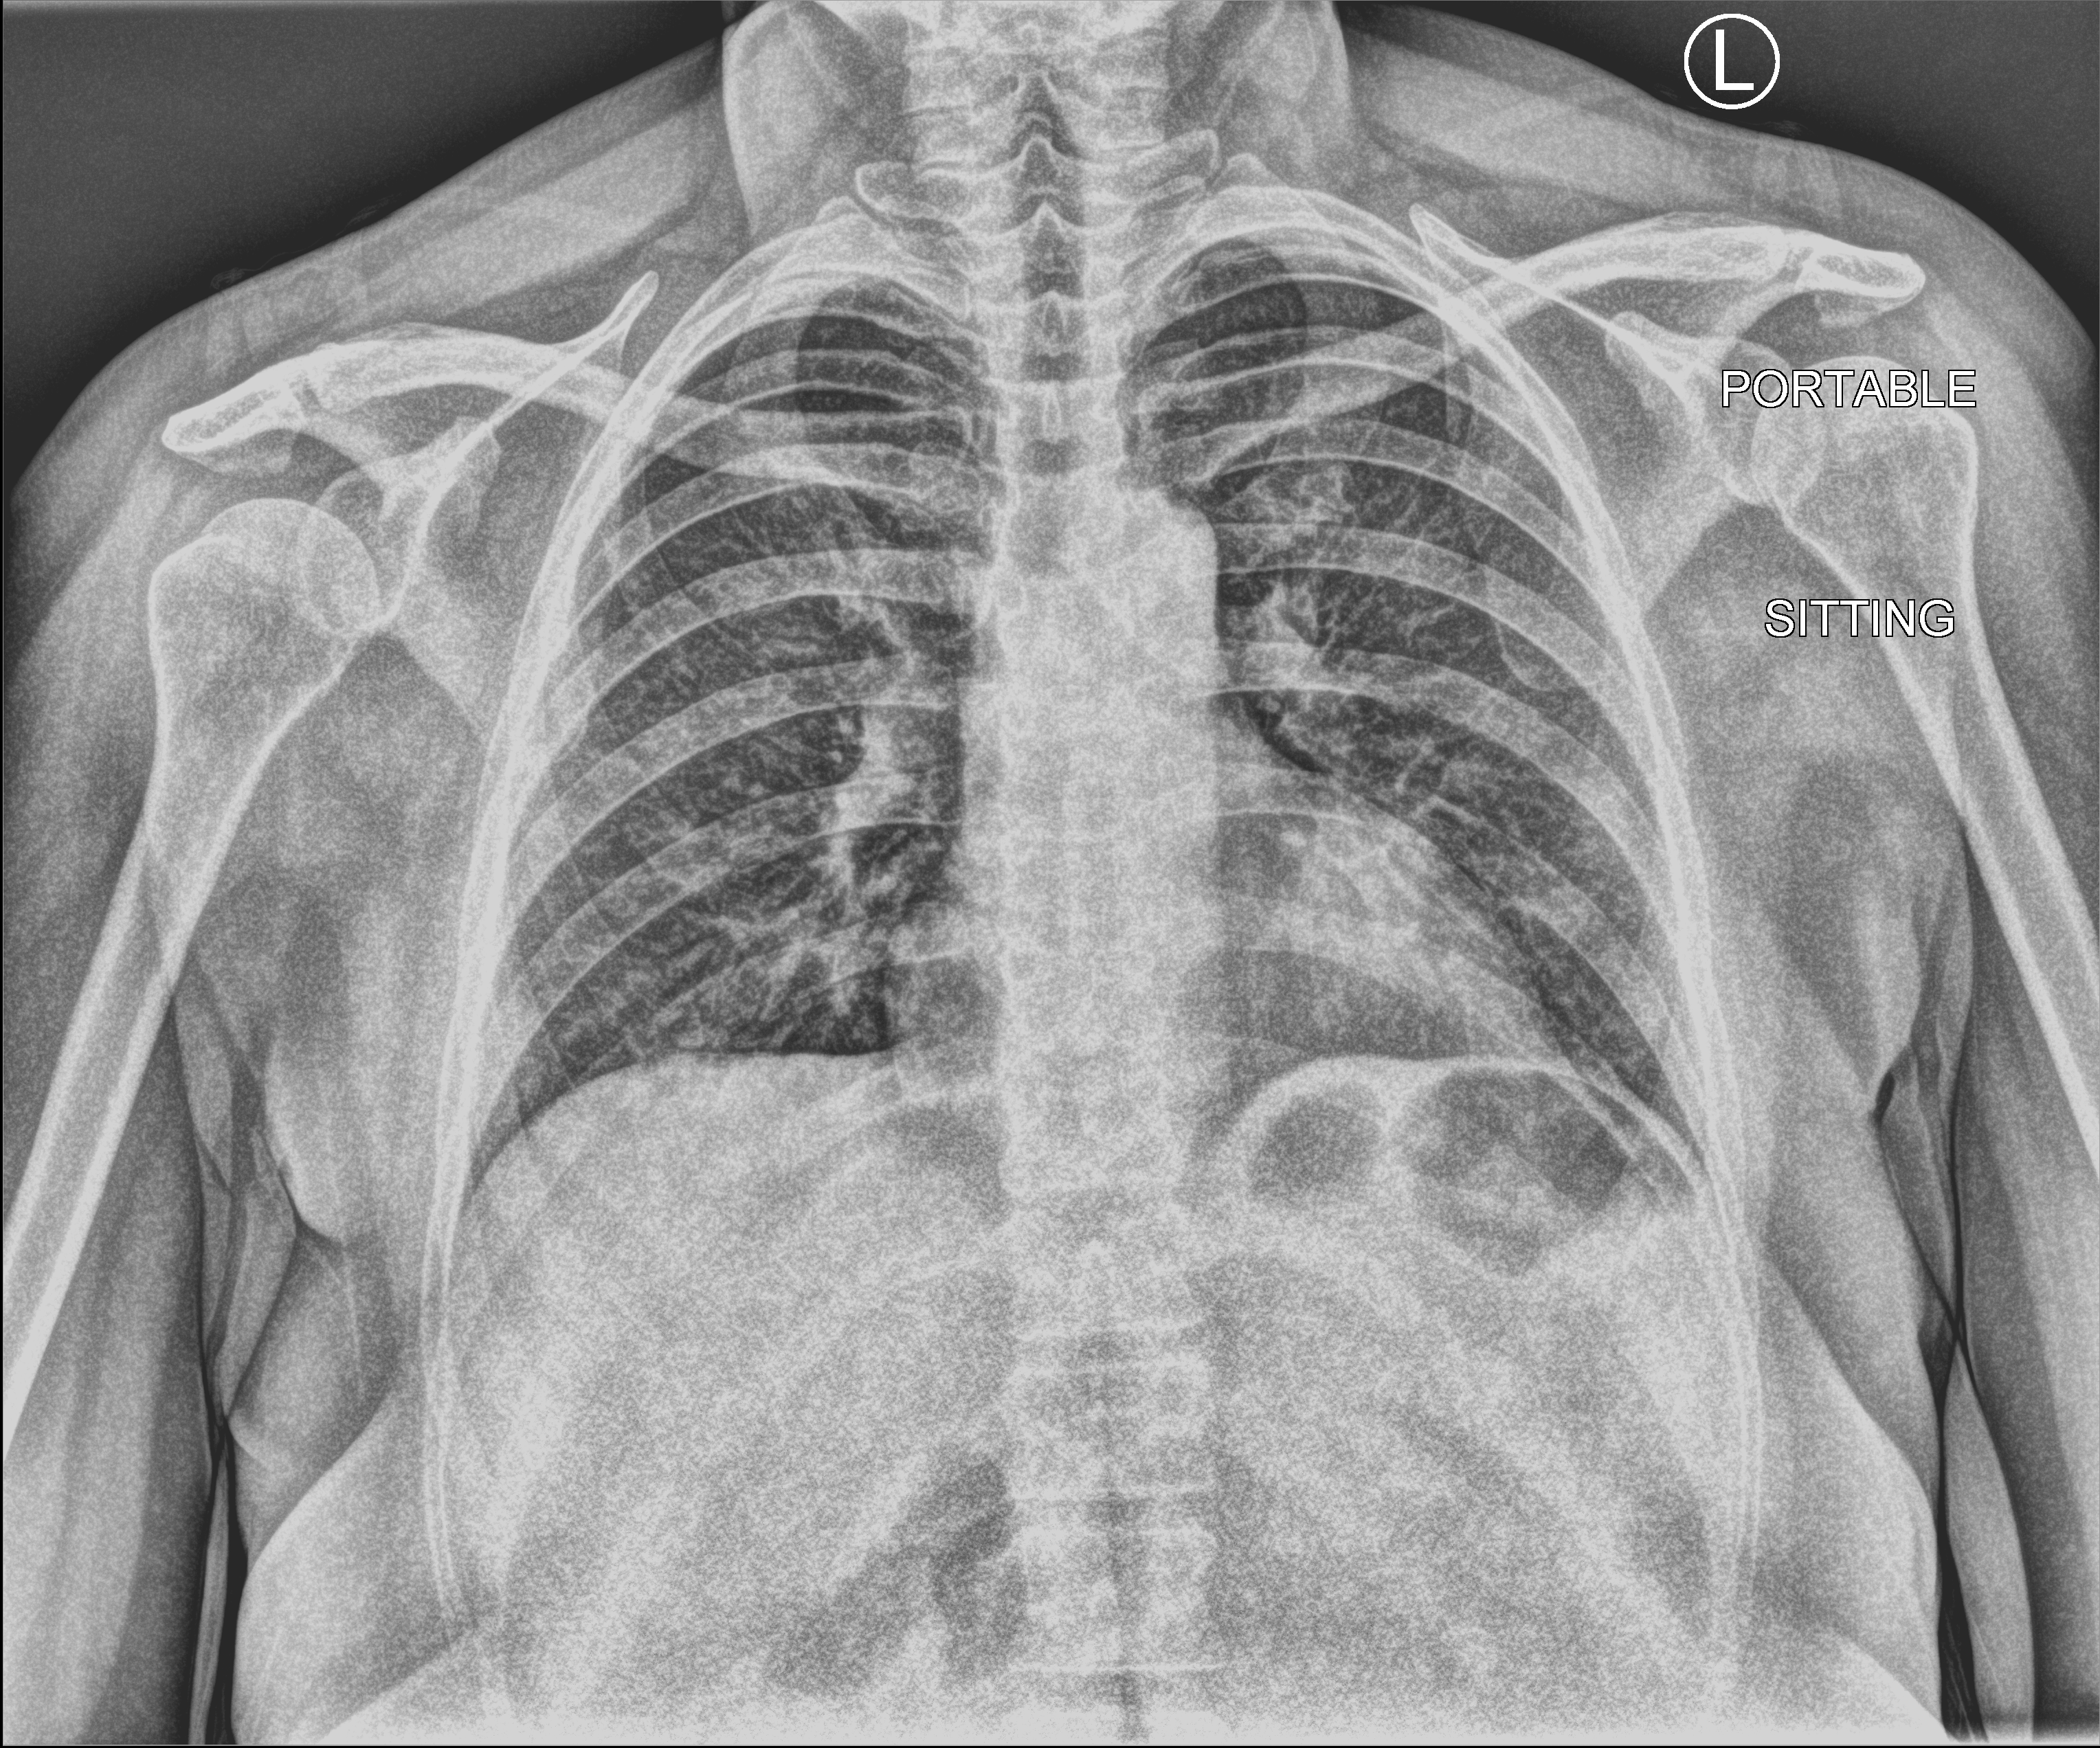
Chest X-ray (portable); anteroposterior (AP) projection. Patient hospitalised with COVID-19; female, aged 18–59 years.
Admission-level facts for this patient (not findings on this image; timing relative to this image not recorded):
- mechanically ventilated during this hospital stay: no
- length of hospital stay: 1 day